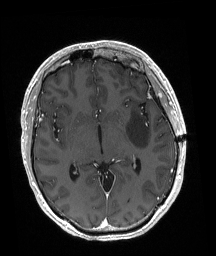
Brain MRI from a brain-tumour surgery series, one axial slice; position 106 of 192 along the scan axis; T1-weighted post-contrast; 1 mm slice thickness; 216 × 256 image matrix, field of view 211 × 250 mm. From the clinical record (not read from this slice): histopathology: Astrocytoma; WHO grade: 3; IDH mutation: yes.
Outlined on this slice (manually delineated by an expert):
- tumour: box from (x=127, y=111) to (x=150, y=149) px